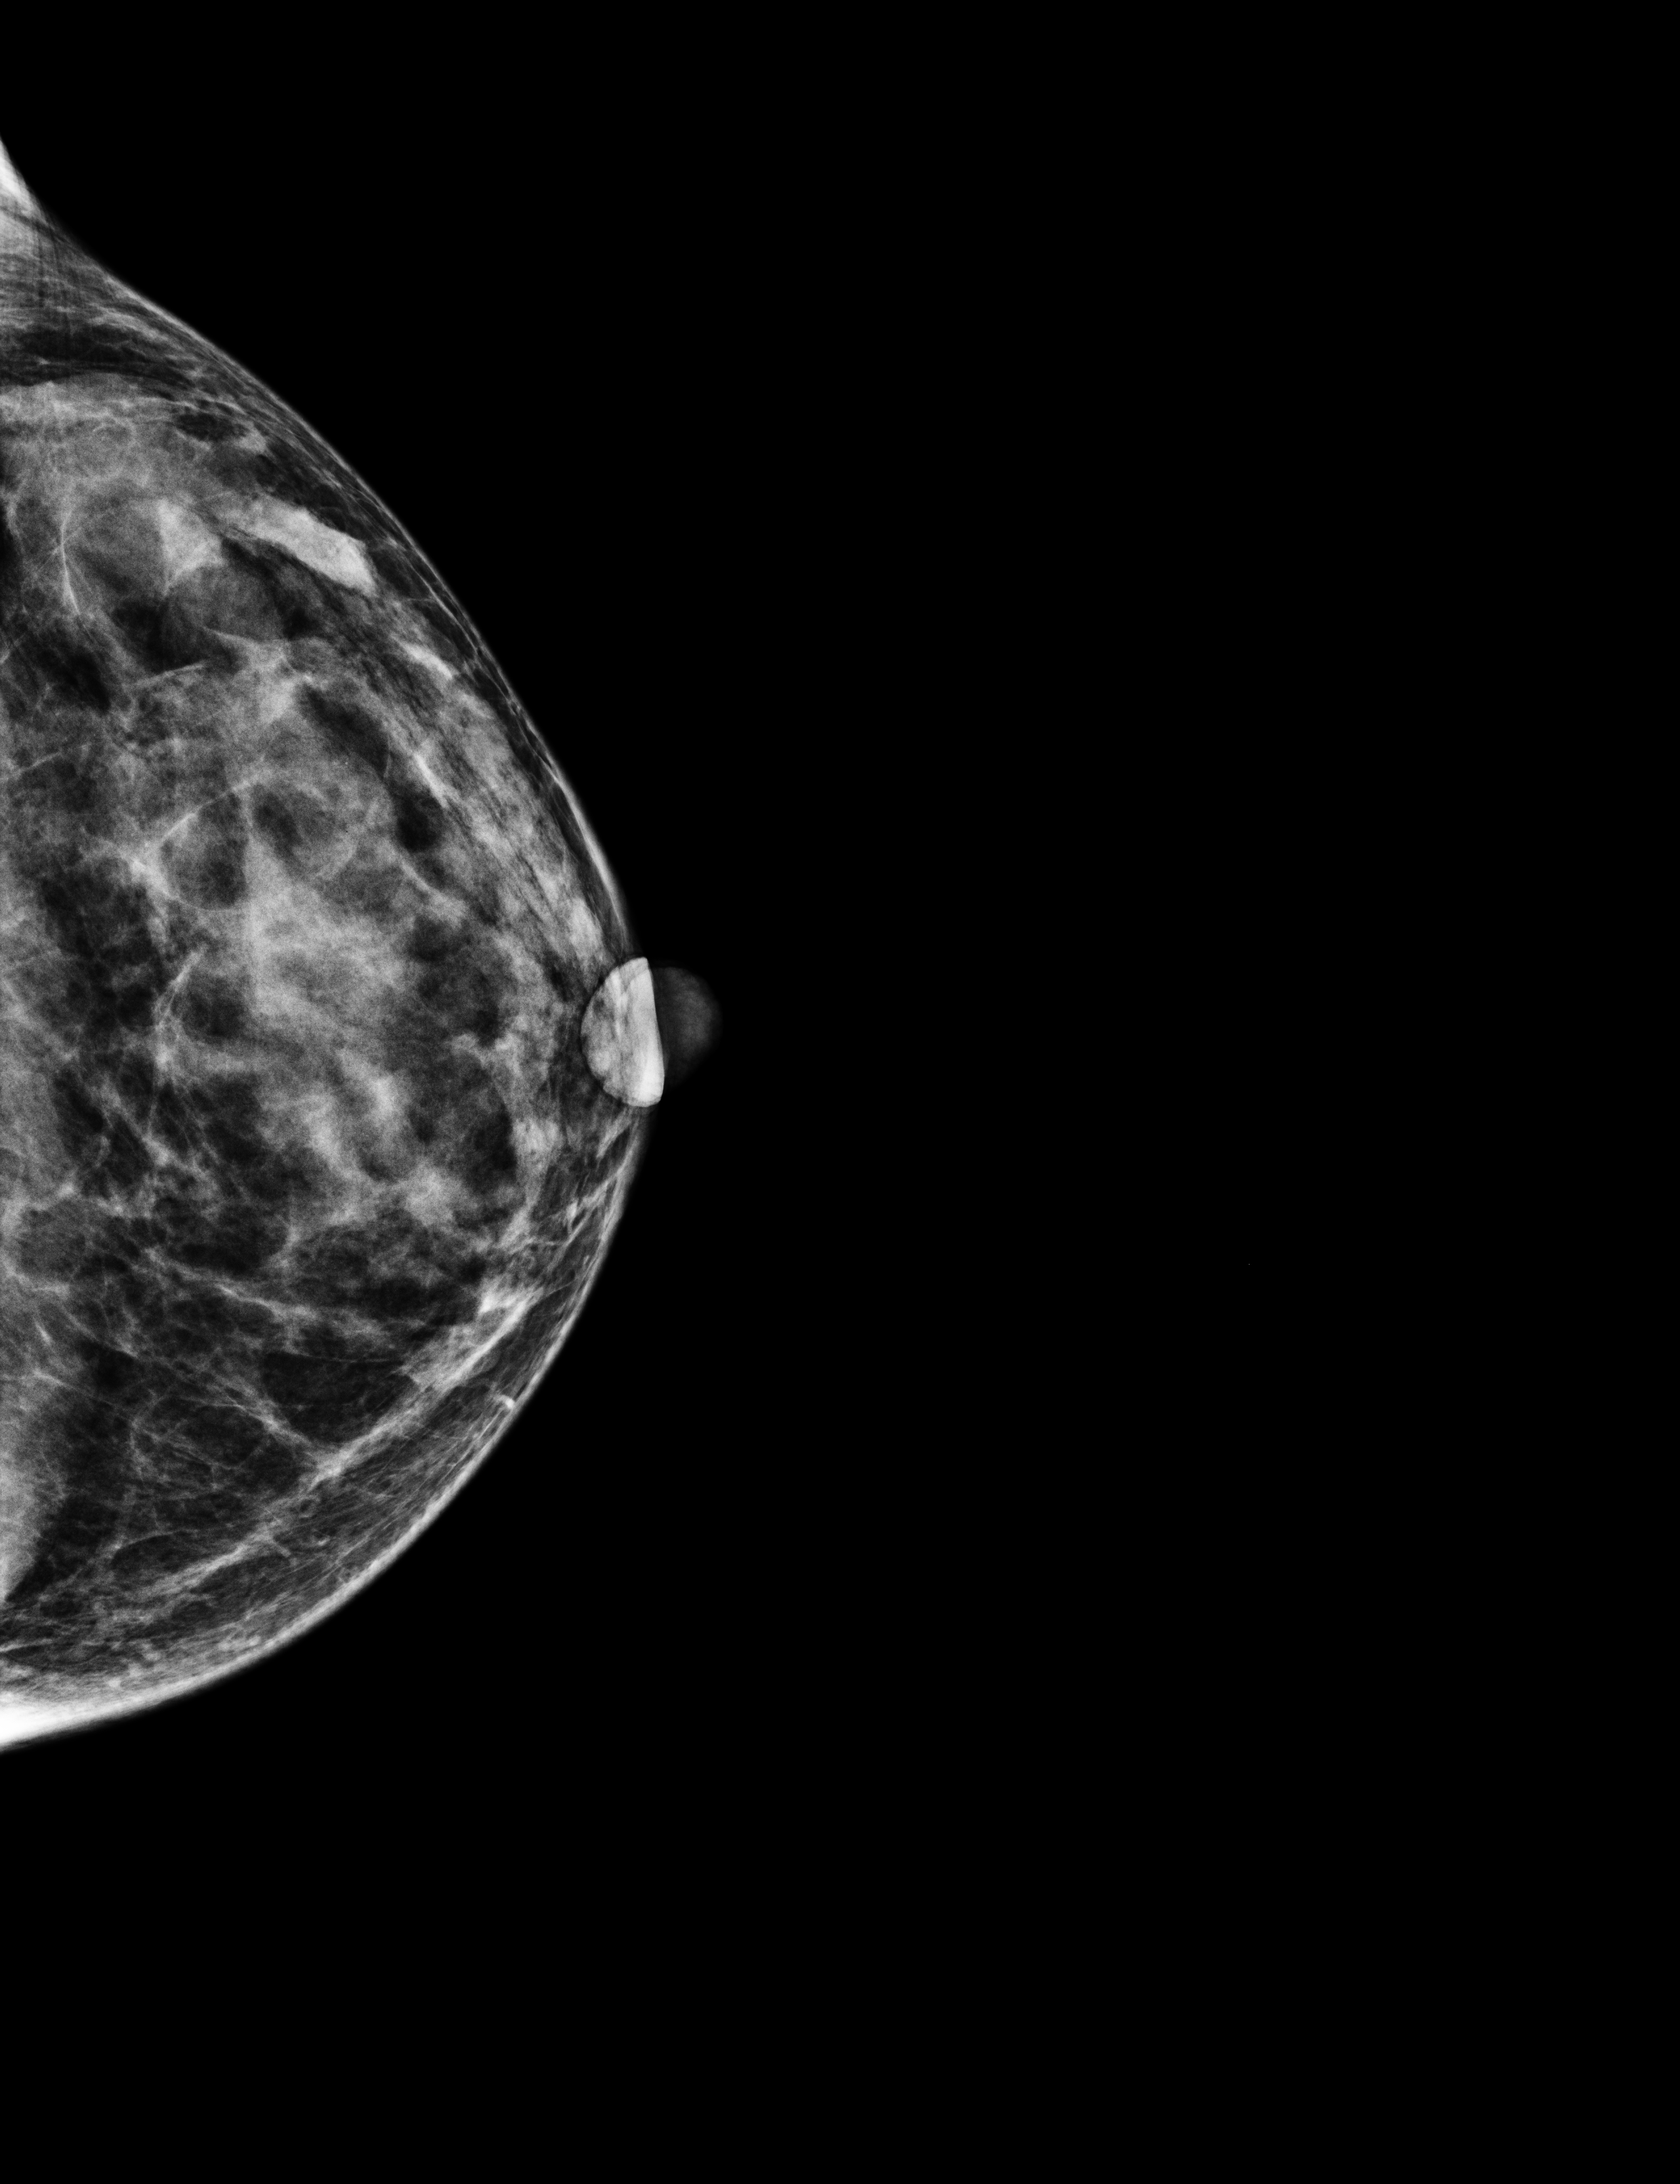
Annual screening mammography examination, compressed breast thickness 37 mm, system: Selenia Dimensions. Female patient, age 54 years.
Image type: full-field digital mammogram. Breast: left. Projection: CC view.